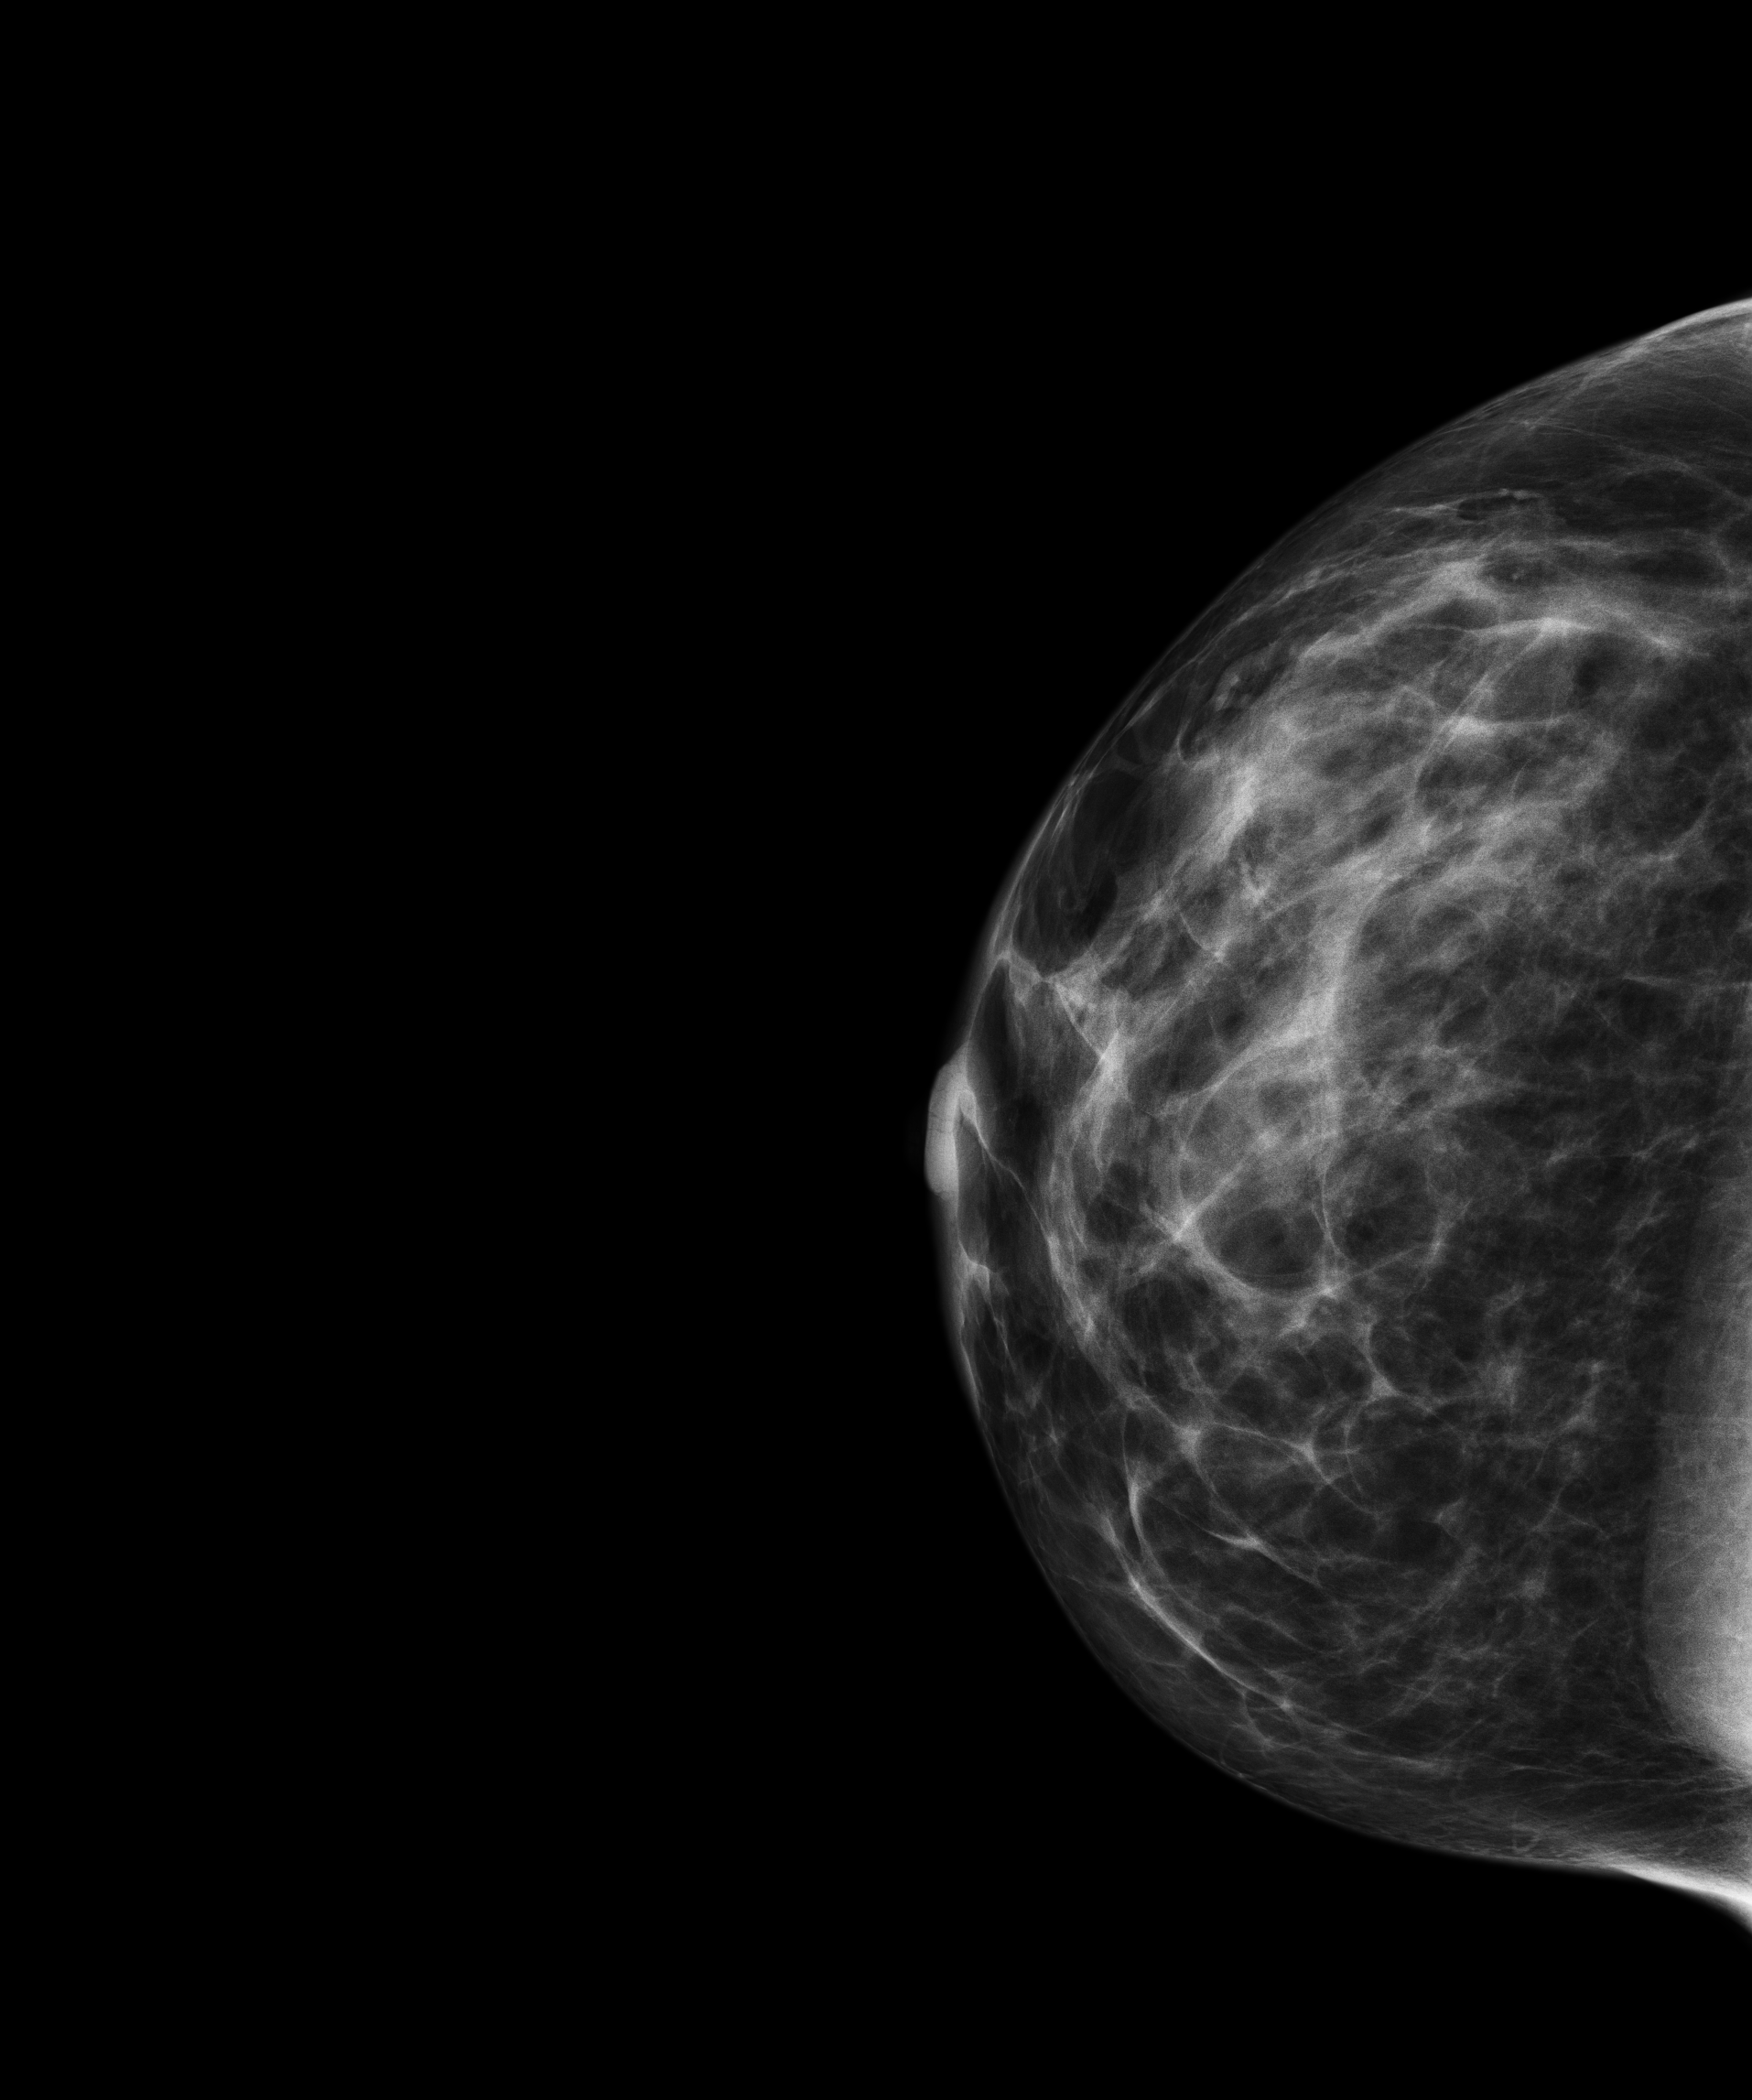
Full-field digital mammogram (FFDM), right breast, CC view, annual screening mammography examination, system: Senographe Essential ADS_56.21.3. Female patient, age 45 years.
Breast density at the screening exam (both breasts): heterogeneously dense (BI-RADS density category c). Final BI-RADS assessment for this screening round (tomosynthesis exam, both breasts): category 1. Recall: no recall after this screen.